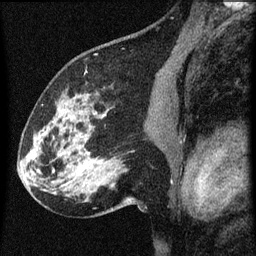
Breast MRI (dynamic contrast-enhanced), one sagittal slice; slice 38 of 60 in the series (ordered by position); dynamic contrast-enhanced series, image 2 of 3 at this slice position (ordered by acquisition); 1.5 T; TE 4.2 ms, TR 8 ms; 2 mm slice thickness; 256 × 256 image matrix, field of view 180 × 180 mm. Female patient, age 61 years.
Structures marked on this image (semi-automatic segmentation, software-assisted and operator-edited):
- analysis volume of interest (the breast-tissue region the enhancement analysis was run in; not a lesion): bounding box <27,82,139,209> (left, top, right, bottom; pixels)
- tumour enhancement mask (voxels above the 70 % enhancement threshold inside the analysis volume of interest): <33,152,98,163>